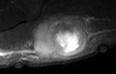
MRI of an extremity soft-tissue mass, one axial slice; slice 21 of 36 in the series (ordered by position); STIR; MR volume resampled by the dataset authors to the PET/CT grid (not the native acquisition matrix); 116 × 74 image matrix, field of view 113 × 72 mm. Male patient. Case-level facts recorded for this patient, not image findings: histological type: pleiomorphic leiomyosarcoma; grade: high; site of the primary tumour: left buttock.
Outlined on this slice (expert contour drawn on MRI and transferred to this co-registered scan by the dataset authors):
- gross tumour volume including surrounding oedema: box from (x=30, y=17) to (x=85, y=57) px
- gross tumour volume (mass): (x=30, y=19)–(x=83, y=57)